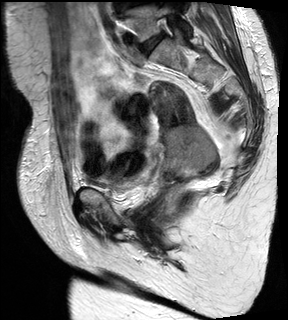
Pelvic MRI for cervical cancer, one sagittal slice; T2-weighted; 1.5 T; TE 89 ms, TR 2740 ms; 4 mm slice thickness; 288 × 320 image matrix. Female patient, age 59 years.
Structures marked on this image (expert manual segmentation):
- uterus and cervix: bounding box [x1, y1, x2, y2] px = [148, 80, 221, 181]